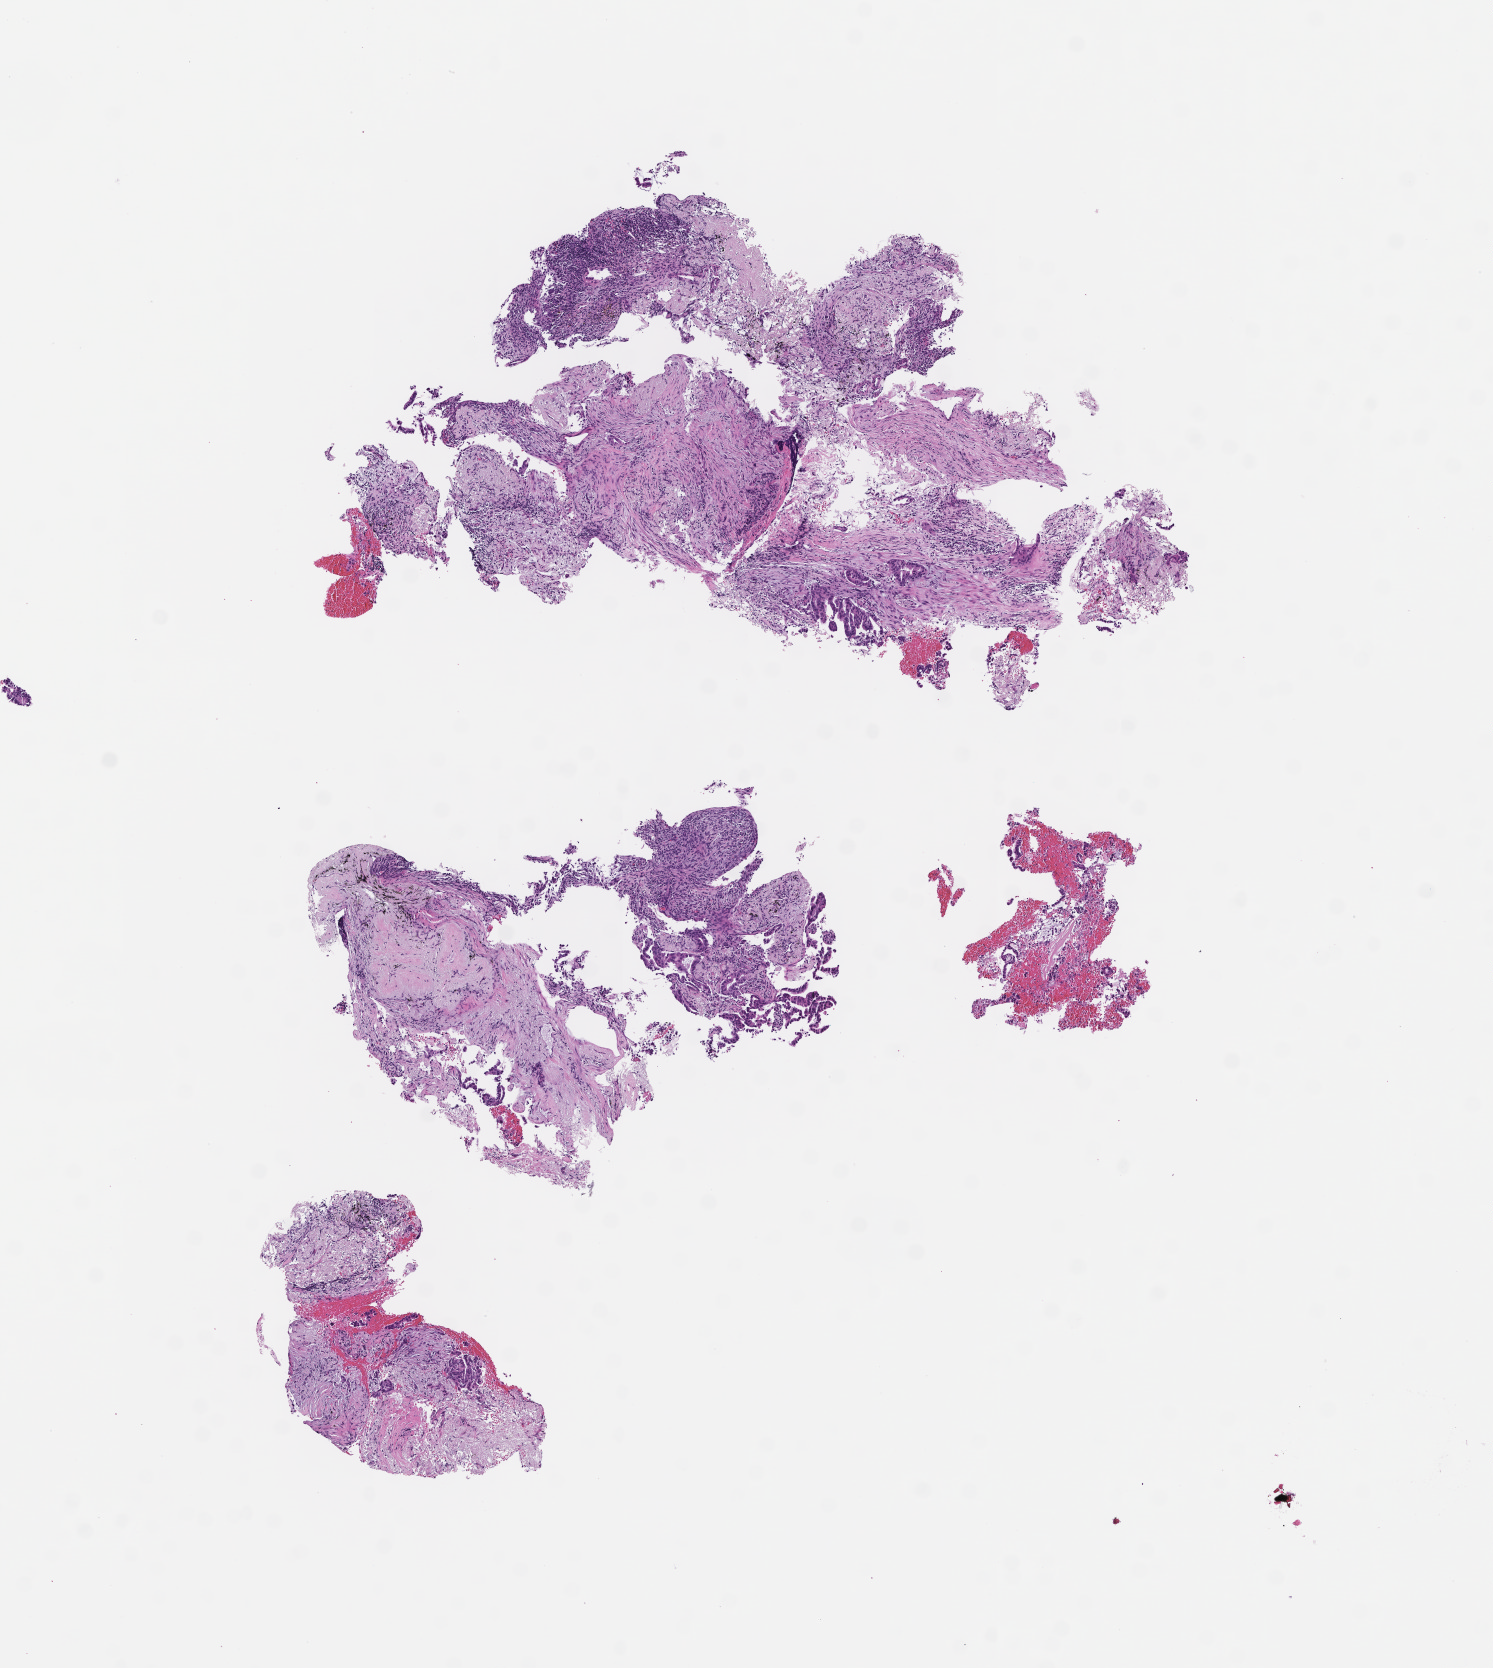
Haematoxylin and eosin whole-slide image, a low-resolution overview of the entire scanned area, about 6.0 x 6.7 mm, formalin-fixed, paraffin-embedded (FFPE) tissue, site: lung, archival tissue. Patient: female.
- this section: primary tumor
- diagnosis: Non-Small Cell Lung Carcinoma